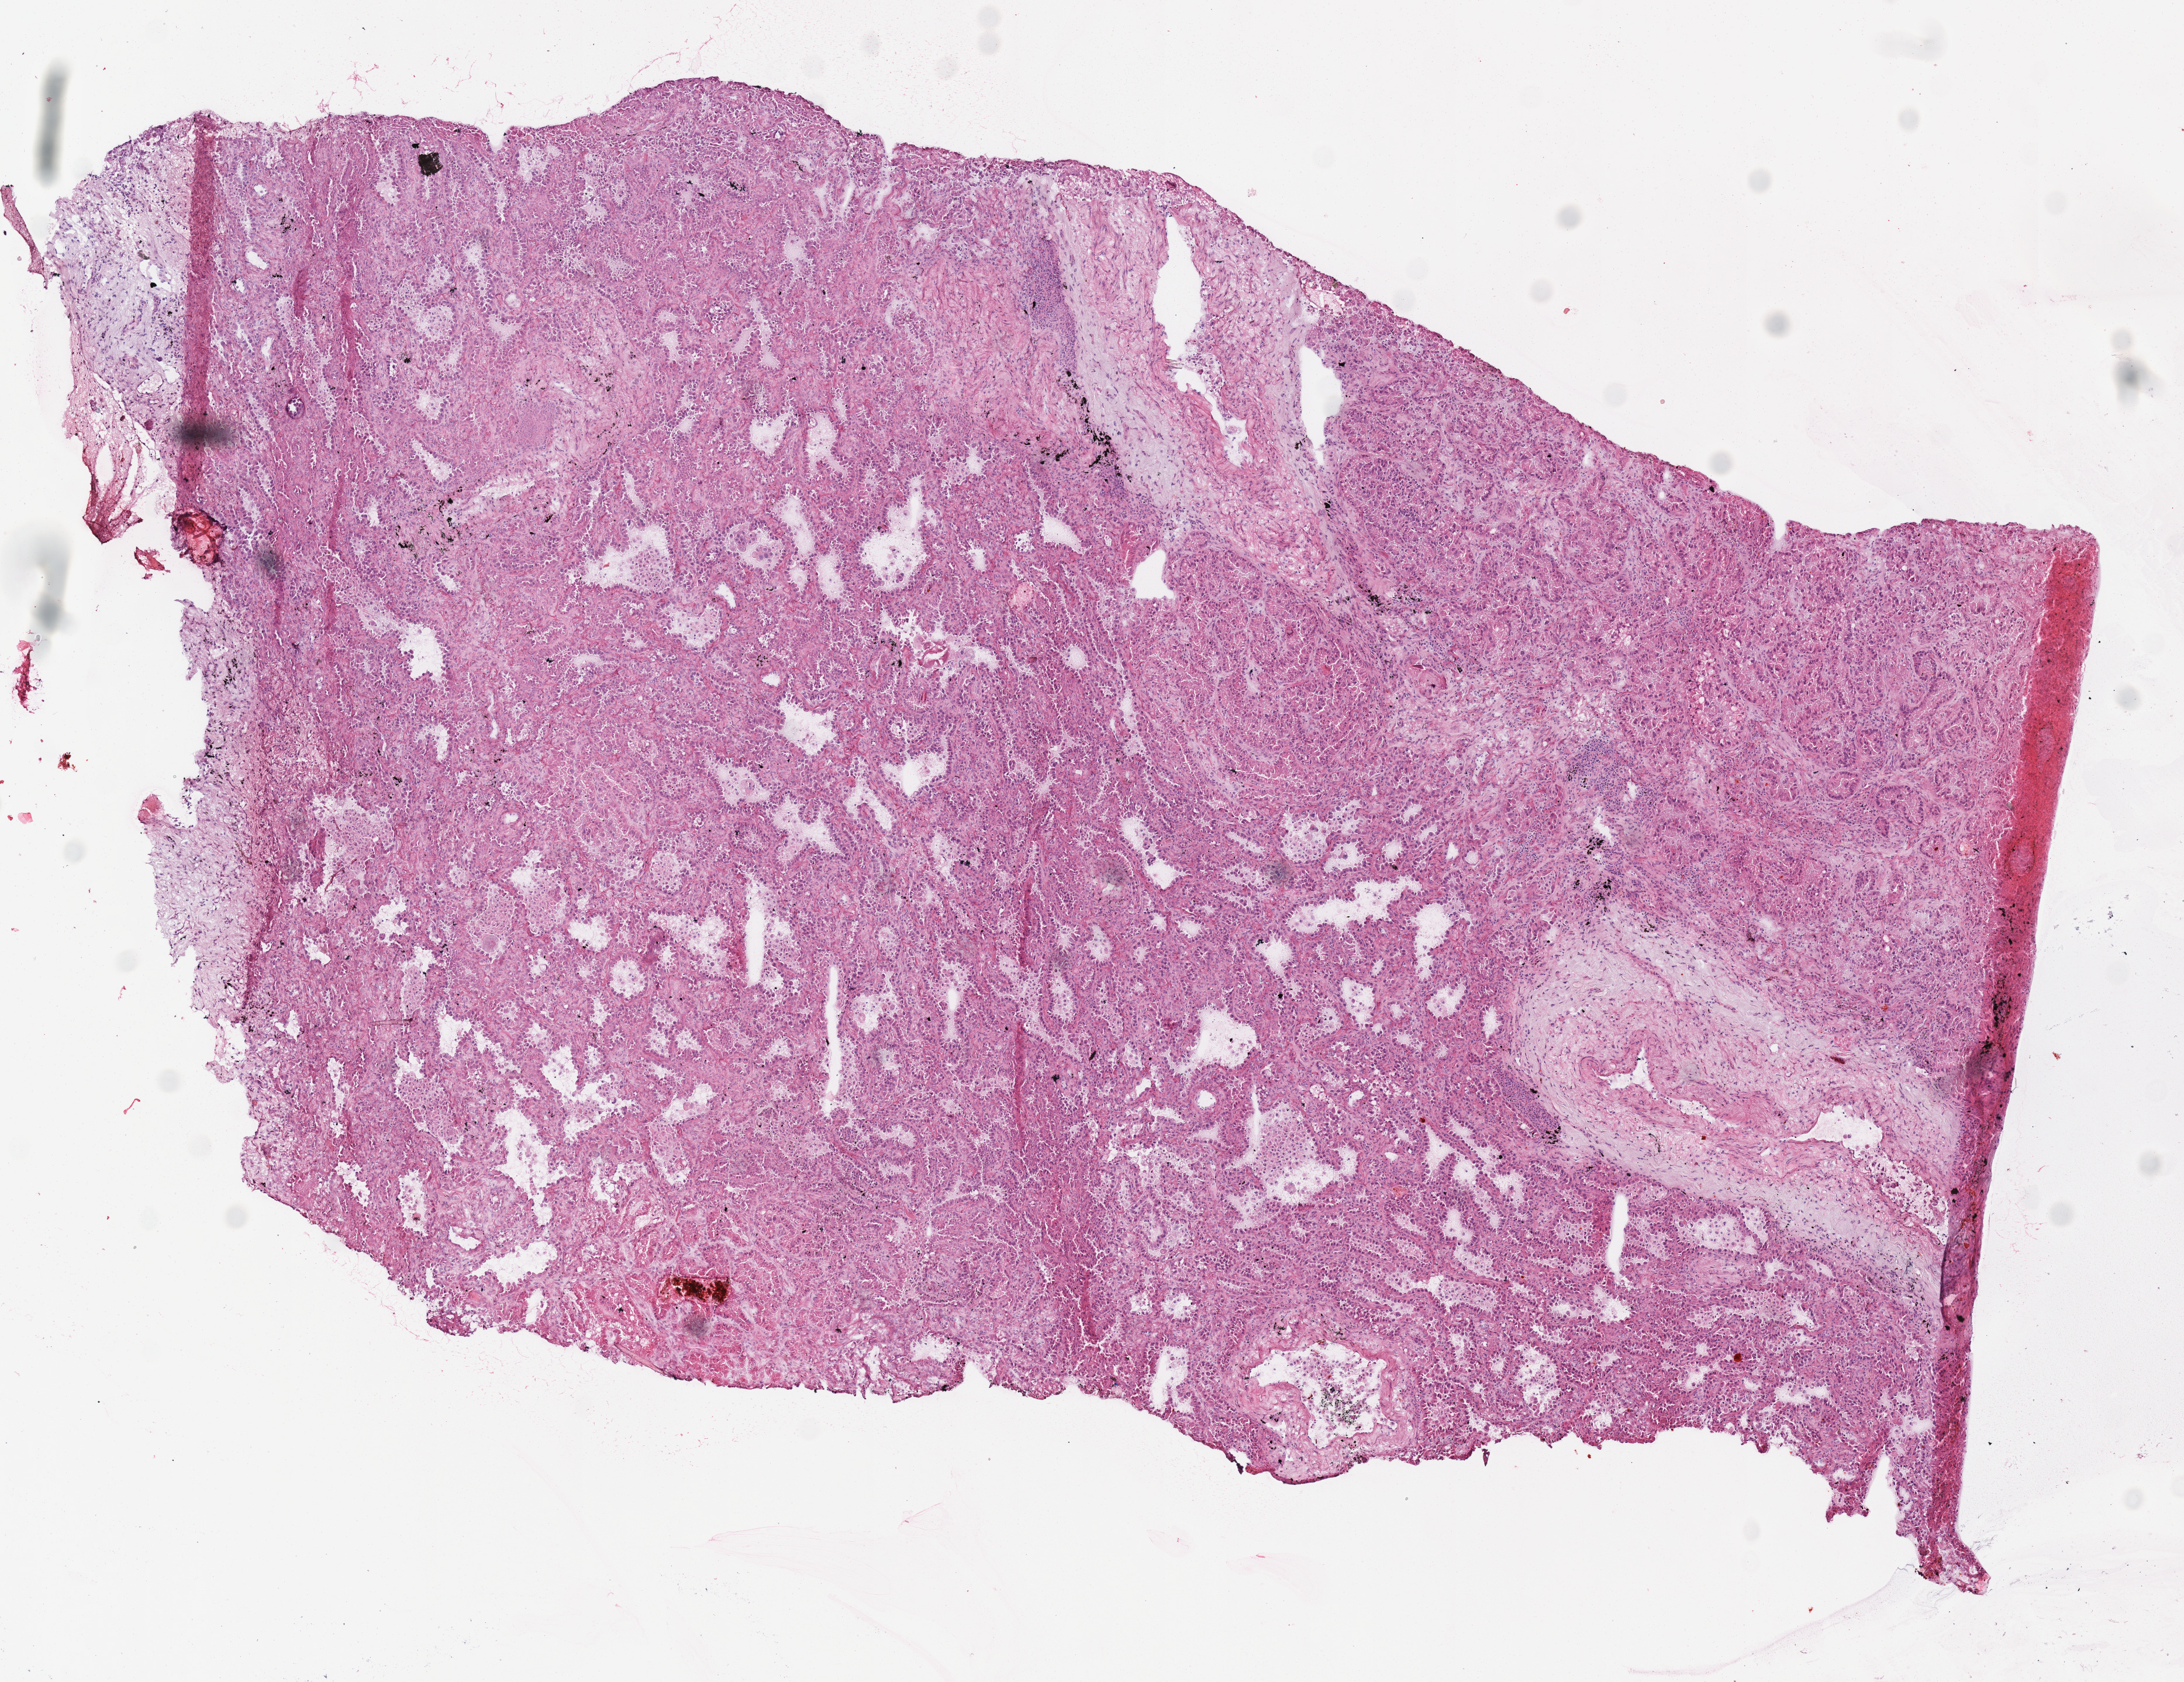
Digitized H&E-stained tissue section (whole slide), whole scanned area (about 7.3 x 5.7 mm, from a 40x scan) shown as a low-resolution overview; frozen section from the top of the tissue portion; sample: primary tumour, lung. Patient: female, age at initial diagnosis 80 years. Pathologist review of this section (percent, as recorded): tumour cells 96%, tumour nuclei 70%, normal cells 0%, stromal cells 4%, necrosis 0%. Infiltration values recorded for this section: lymphocyte infiltration 5%, monocyte infiltration 3%.
AJCC pathologic stage: IIB (6th edition). Laterality: right. Pathologic diagnosis: Adenocarcinoma with mixed subtypes.